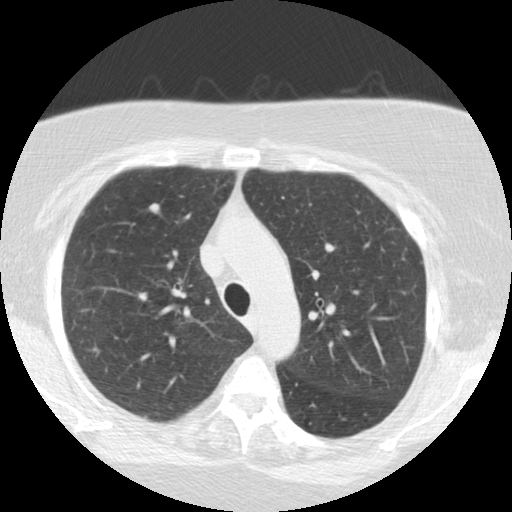
Low-dose screening chest CT, one axial slice; position 171 of 225 along the scan axis; lung window (W 1500 / L -600 HU); 2.5 mm slice thickness; 512 × 512 image matrix, field of view 320 × 320 mm.
Outlined on this slice (expert manual segmentation):
- lesion 1 (tumor, upper lobe of right lung): bounding box (x1, y1, x2, y2) in pixels: (149, 203, 160, 214)